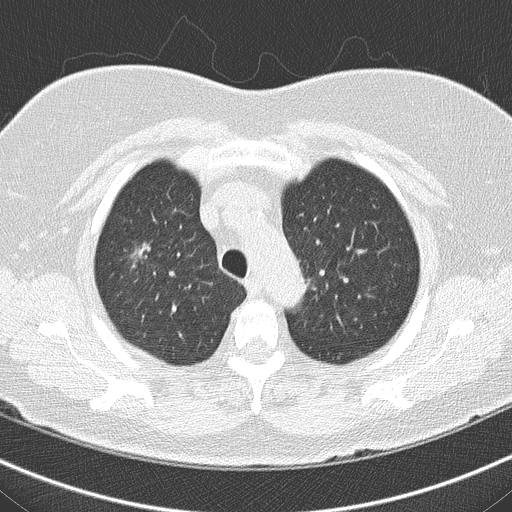
Low-dose screening chest CT, axial slice, third screening round (two years after baseline), lung window (W 1500 / L -600 HU), lung (sharp) reconstruction kernel (B50f), slice 137 of 161 in the series, 512 × 512 image matrix. Female participant, aged 74 years at enrolment. Former smoker at enrolment.
Expert-annotated lung lesion, bounding box <111,232,179,296> (left, top, right, bottom; pixels). The screening reader recorded 5 non-calcified nodules or masses ≥4 mm on this exam (right upper lobe, right middle lobe, right middle lobe, left lower lobe, right lower lobe); which of them this box marks is not recorded. Official screen result: positive, other. Participant outcome: lung cancer diagnosed 117 days after this screen — bronchiolo-alveolar carcinoma, non-mucinous, right upper lobe, well differentiated (G1), stage IA (AJCC 6th edition), 14 mm at pathology.